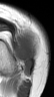
MRI of an extremity soft-tissue mass, one axial slice; MR volume resampled by the dataset authors to the PET/CT grid (not the native acquisition matrix); 3.27 mm slice thickness; 54 × 97 image matrix, field of view 53 × 95 mm. Female patient. Case-level facts recorded for this patient, not image findings: histological type: spindle cell suggestive of biphasic synovial sarcoma; grade: intermediate; site of the primary tumour: left knee.
Annotated regions visible in this slice (expert contour drawn on MRI and transferred to this co-registered scan by the dataset authors):
- gross tumour volume including surrounding oedema: box from (x=14, y=34) to (x=36, y=77) px
- gross tumour volume (mass): (x=14, y=39)–(x=36, y=77)